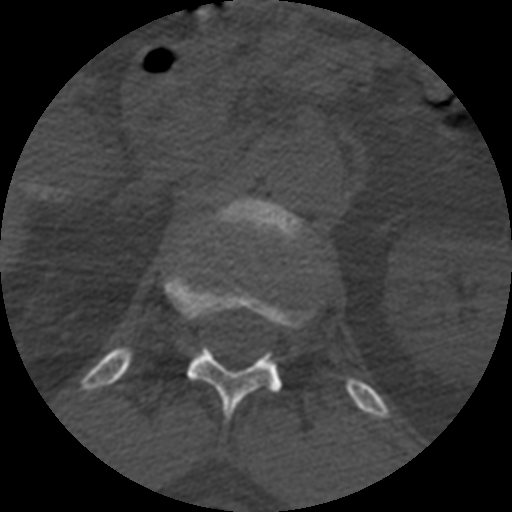
CT including the spine, one axial slice. Reconstruction kernel STANDARD. 120 kVp. Bone window (W 1800 / L 400 HU). 1.25 mm slice thickness. 512 × 512 image matrix, field of view 160 × 160 mm. Patient age 71 years. Case-level facts recorded for this patient, not image findings: primary cancer: prostate.
Outlined on this slice (semi-automatically segmented with operator editing):
- L1 vertebra: bounding box (x1, y1, x2, y2) in pixels: (209, 200, 309, 245)
- T12 vertebra: (165, 272, 312, 421)